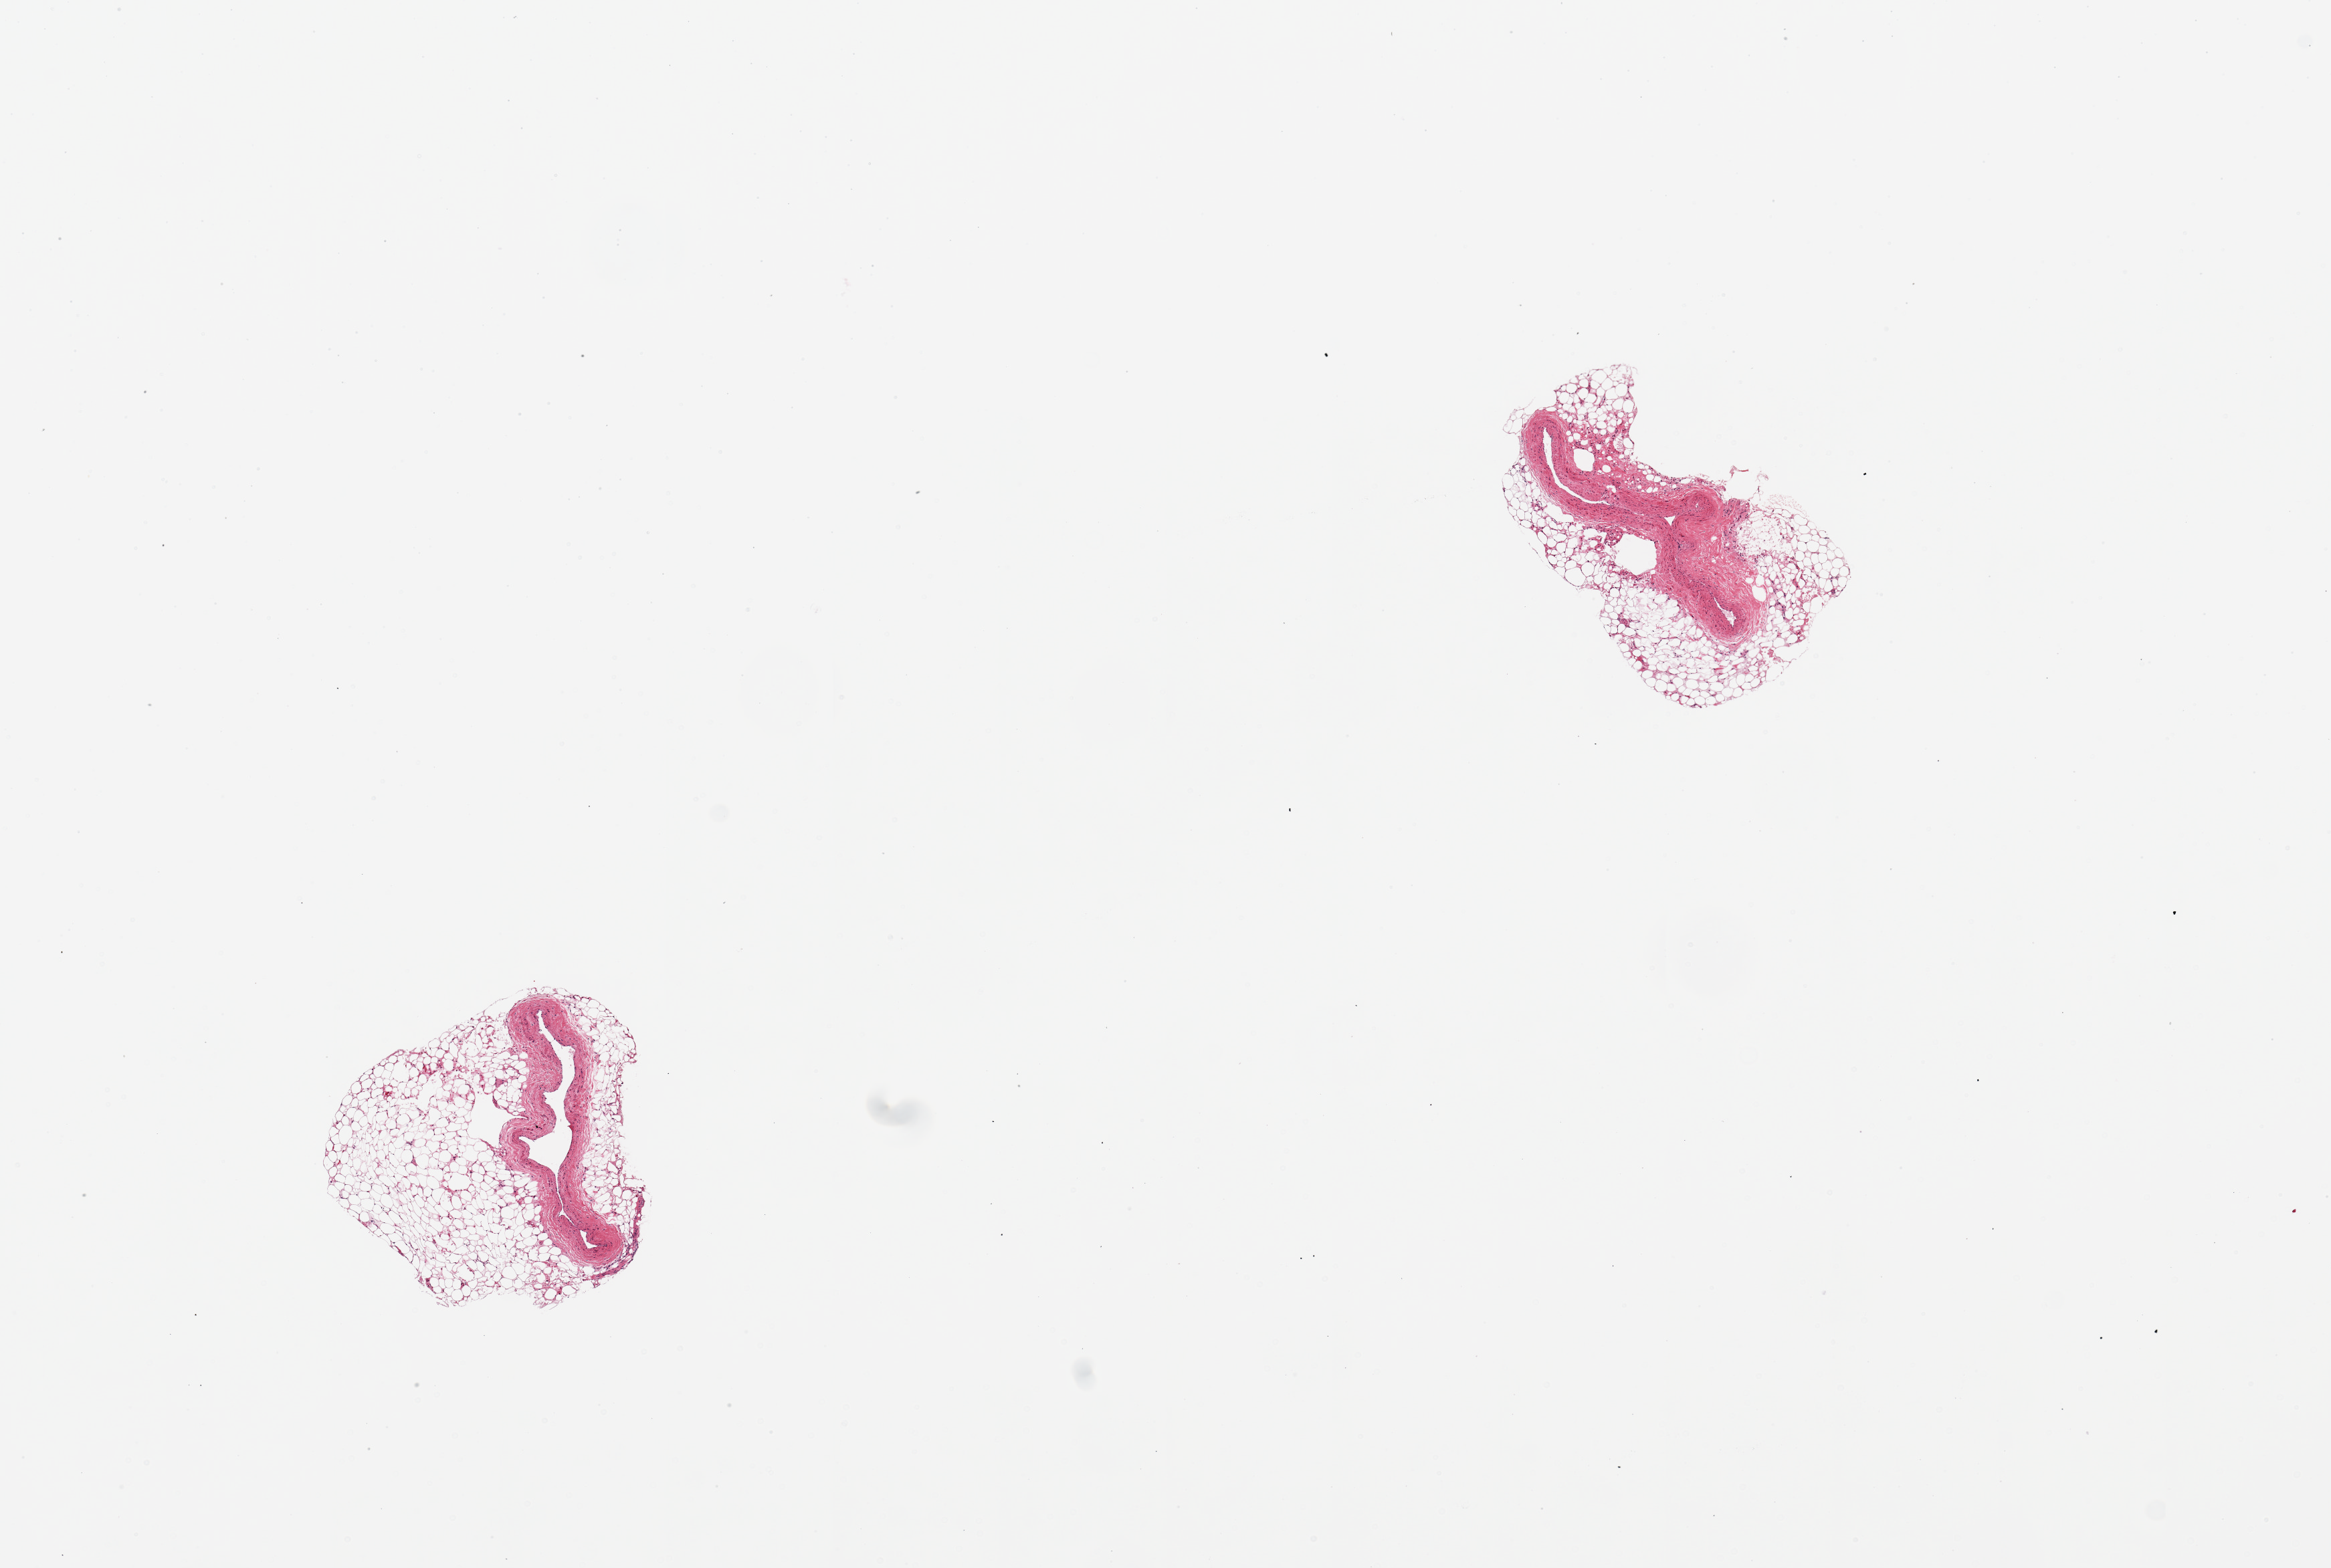
Digitized H&E-stained section, brightfield, a low-resolution overview of the entire scanned area, about 13.8 x 9.3 mm. PAXgene-fixed, paraffin-embedded tissue. Sampled site (target tissue): coronary artery. Tissue donor sample. Donor: female.
• reviewer comment on this tissue sample: 2 pieces; no plaques; both surrounded by excessive fat, up to 1 mm thick